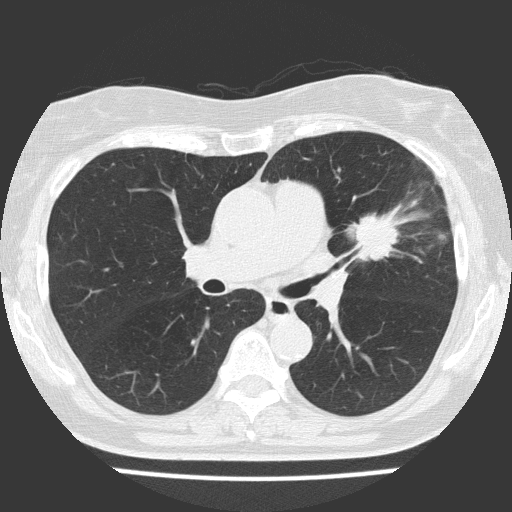
Low-dose screening chest CT, axial slice. Baseline annual screen. Lung window (W 1500 / L -600 HU). 2 mm slice thickness. Slice 65 of 151 in the series. Female participant, aged 70 years at enrolment. Current smoker at enrolment.
Expert-annotated lung lesion, bounding box <326,190,433,281> (left, top, right, bottom; pixels). The screening reader recorded 2 non-calcified nodules or masses ≥4 mm on this exam (left upper lobe, right upper lobe); which of them this box marks is not recorded. Lung cancer was diagnosed 25 days after this screen: adenocarcinoma, NOS, left upper lobe, poorly differentiated (G3), stage IV (AJCC 6th edition), 30 mm at pathology.